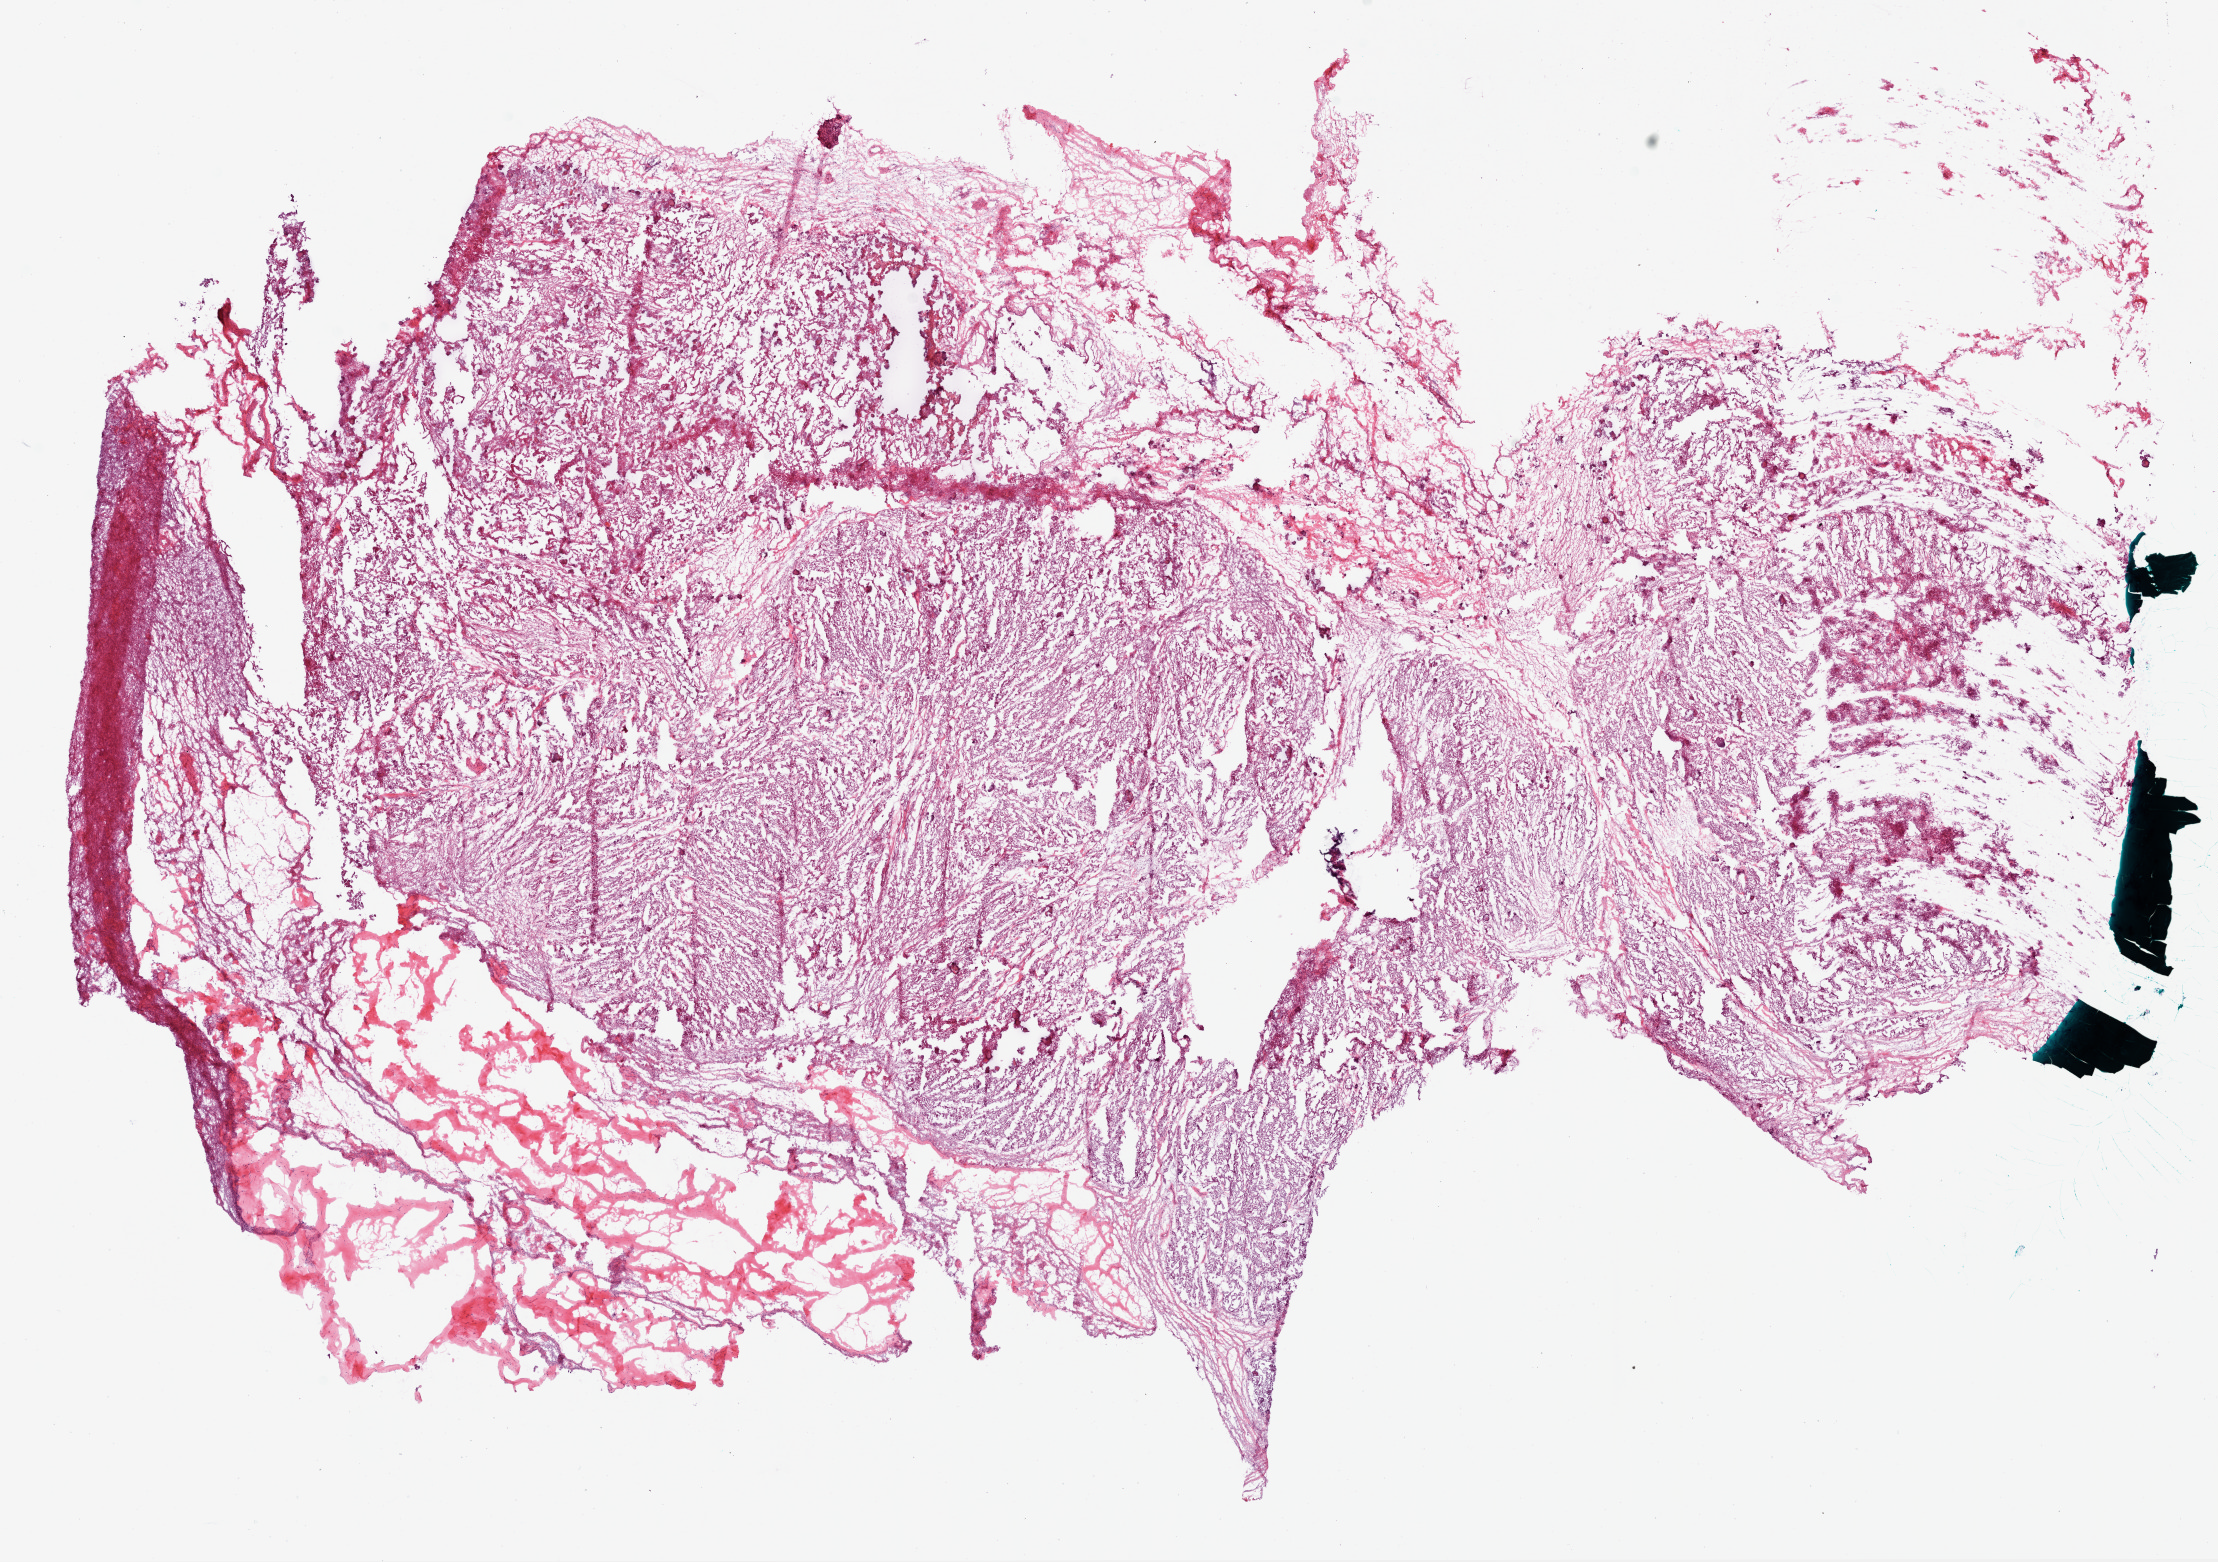
Digitized Hematoxylin and eosin (H&E) stained tissue section (whole slide) — low-resolution overview of the scanned area, about 17.9 x 12.6 mm. Frozen section from the bottom of the tissue portion. Ovary, primary tumour sample. Female patient; age at initial diagnosis 38 years. Histologic grade: G3 (poorly differentiated). Composition of this section per pathologist review: tumour cells 70%, tumour nuclei 95%, stromal cells 10%, necrosis 20%.
* FIGO stage: IIIC
* histologic diagnosis: Serous cystadenocarcinoma, NOS
* laterality: bilateral